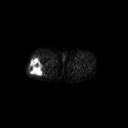
FDG PET of an extremity soft-tissue mass (from a PET/CT study), one axial slice; position 253 of 267 along the scan axis; 128 × 128 image matrix, field of view 700 × 700 mm. Male patient, age 43 years. Case-level facts recorded for this patient, not image findings: histological type: poorly differentiated synovial sarcoma; grade: high; site of the primary tumour: right buttock.
Outlined on this slice (expert contour drawn on MRI and transferred to this co-registered scan by the dataset authors):
- gross tumour volume including surrounding oedema: bounding box [x1, y1, x2, y2] px = [28, 57, 46, 76]
- gross tumour volume (mass): [28, 57, 46, 76]